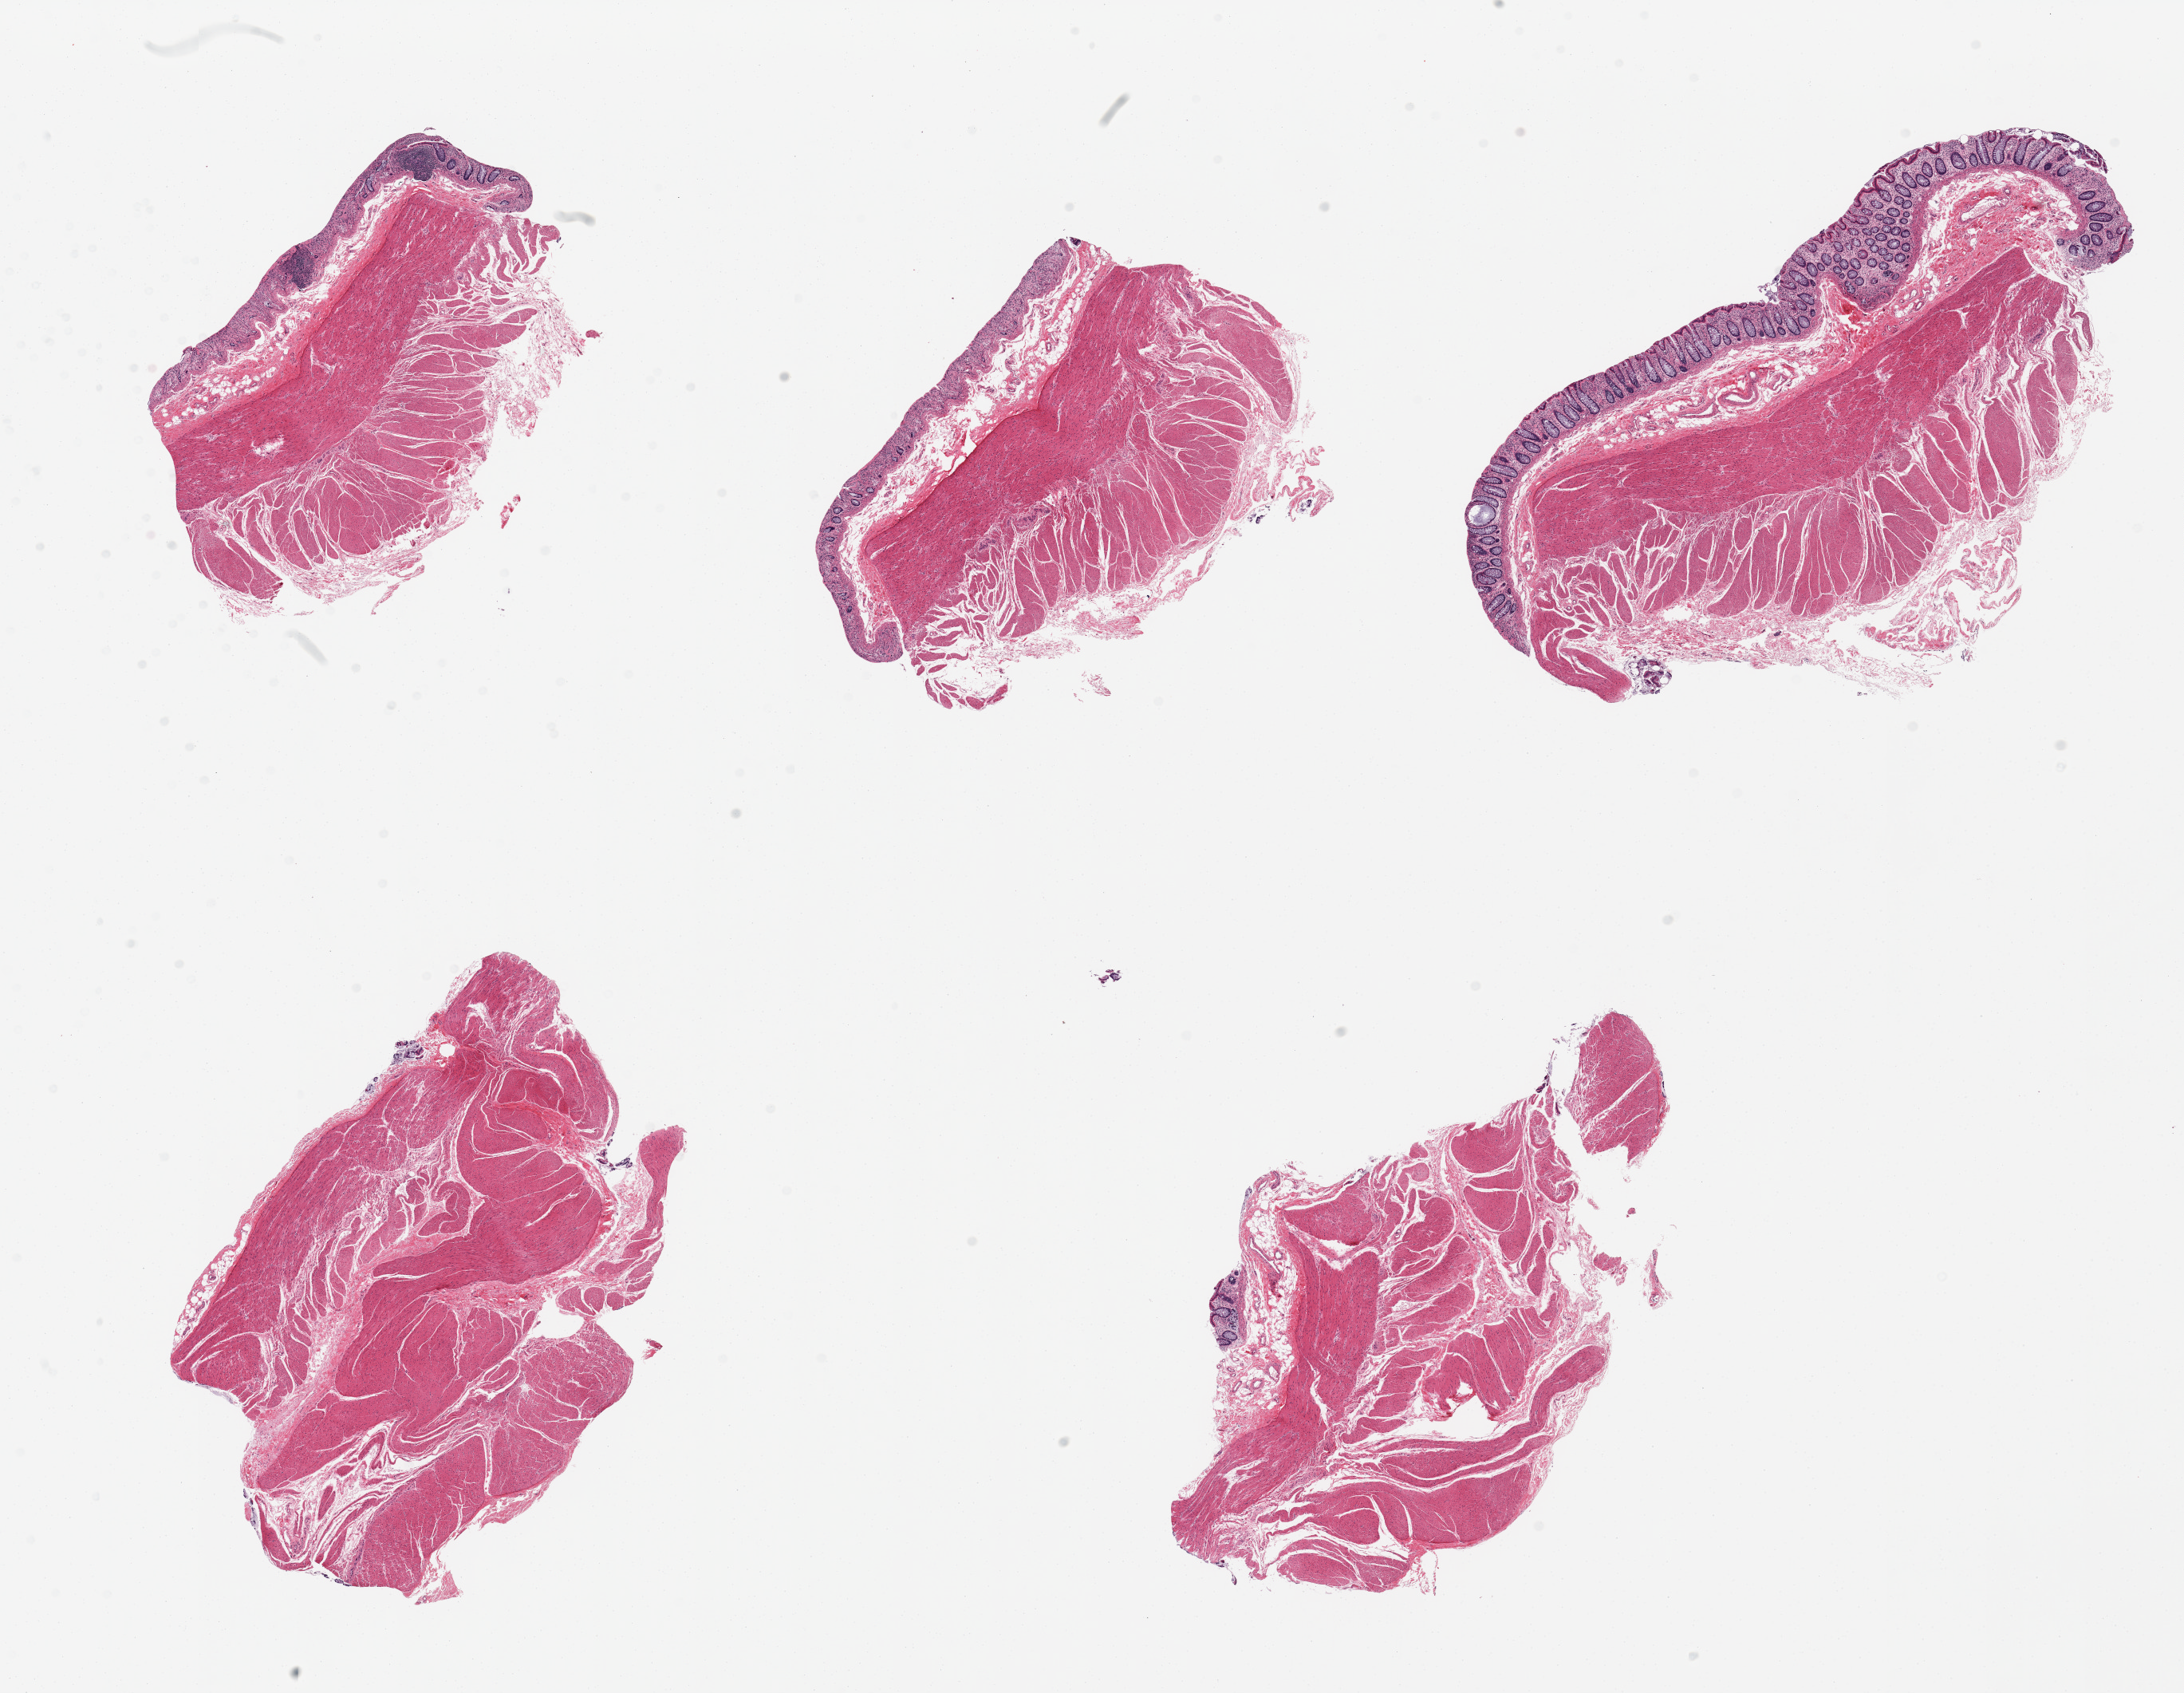
Digitized haematoxylin and eosin-stained section, brightfield — whole scanned area (about 21.7 x 16.8 mm, slide scanned at 20x) shown as a low-resolution overview, PAXgene-fixed, paraffin-embedded tissue, target tissue: sigmoid colon, donor tissue sample. Male donor.
Review note (as recorded): 6 pieces; 3 are full thickness (mucosa not target).